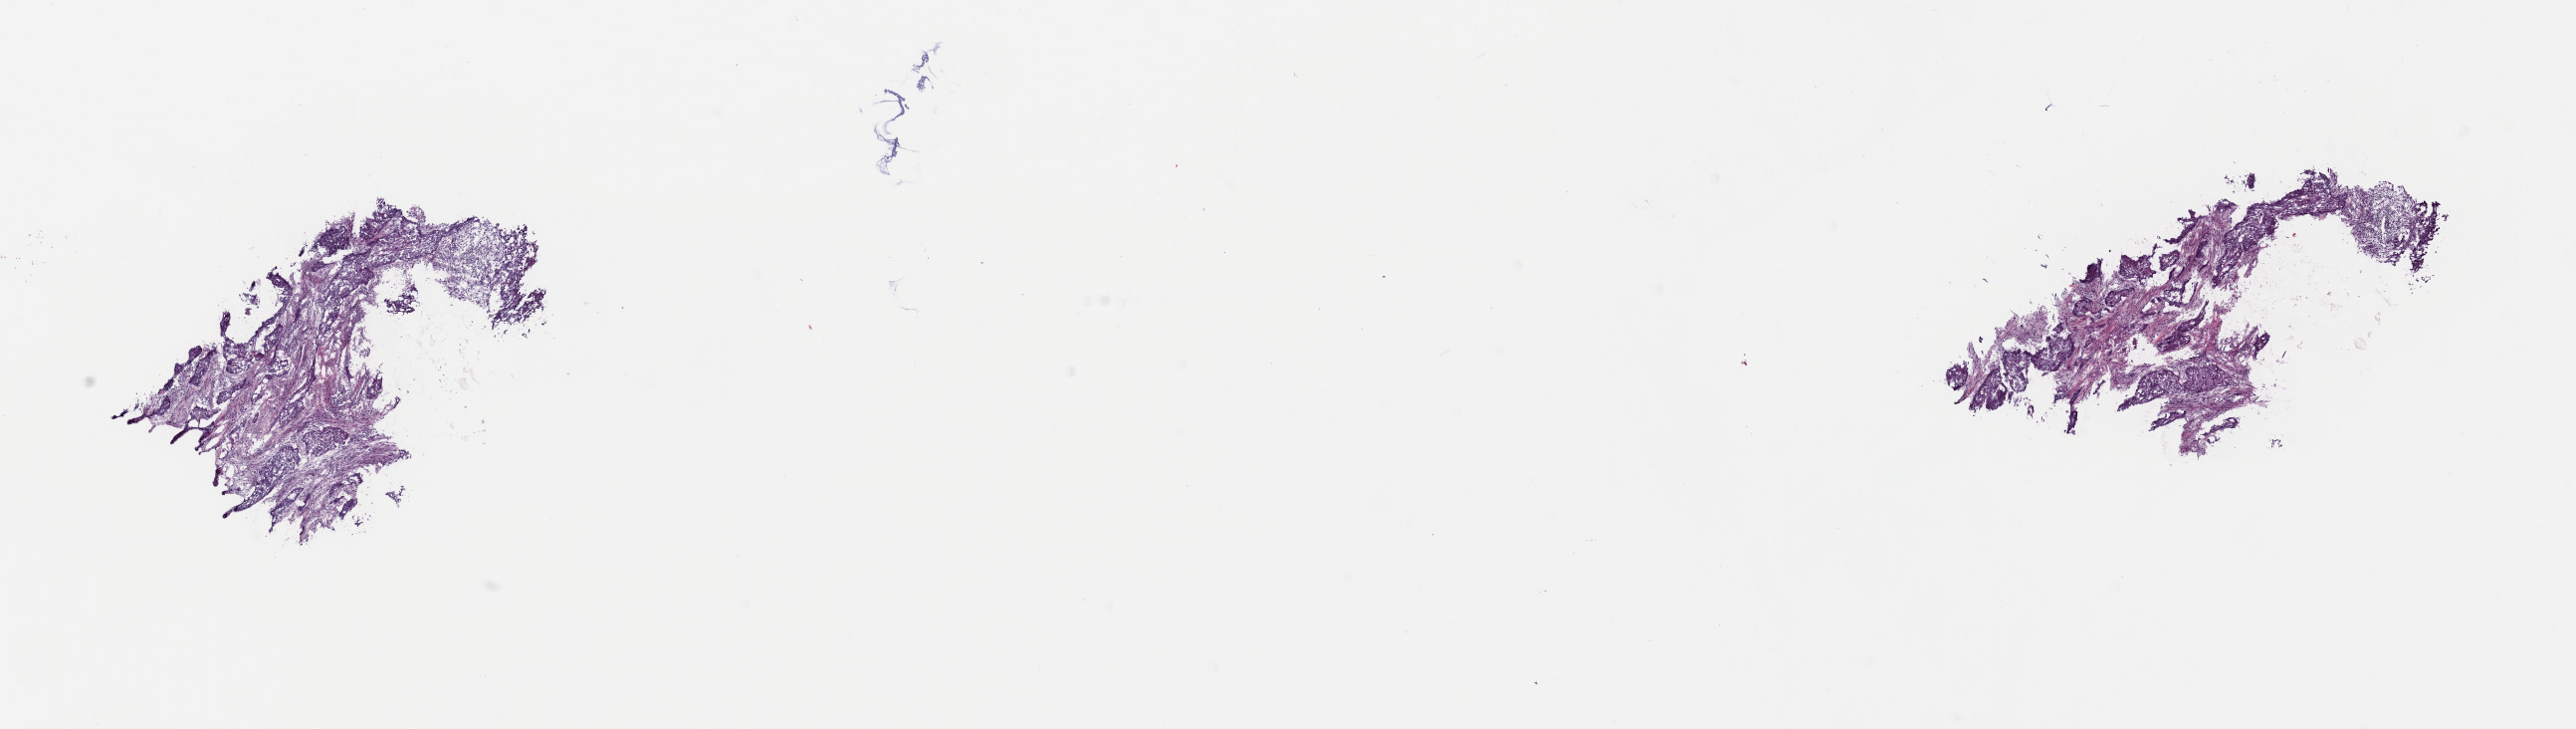
Hematoxylin and eosin (H&E) stained whole-slide image — whole scanned area (about 20.4 x 5.8 mm, from a 40x scan) shown as a low-resolution overview, frozen section from the top of the tissue portion, primary tumour sample from the bladder. Patient: male, age at initial diagnosis 65 years. Histologic grade: high grade. Slide review estimates, as recorded: tumour cells 100%, tumour nuclei 65%, normal cells 0%, stromal cells 0%, necrosis 0%. Infiltration values recorded for this section: lymphocyte infiltration 3%, monocyte infiltration 0%, neutrophil infiltration 0%.
- histologic diagnosis: Transitional cell carcinoma (anterior wall of bladder)
- AJCC pathologic stage: III